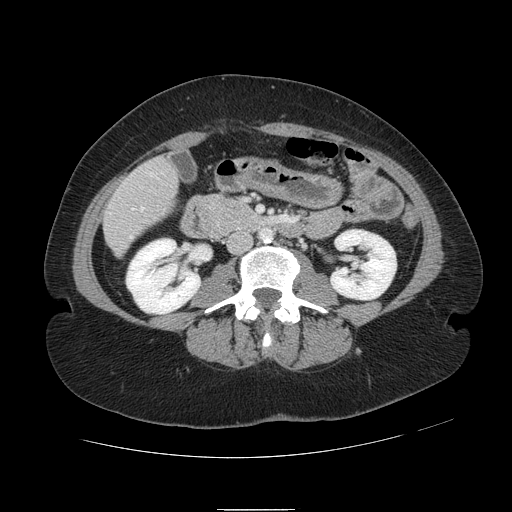
Contrast-enhanced abdominal CT, one axial slice; slice 20 of 121 in the series (ordered by position); 120 kVp; intravenous contrast given; soft-tissue window (W 400 / L 40 HU); 2.5 mm slice thickness; 512 × 512 image matrix, field of view 400 × 400 mm. Female patient, age 52 years. Case-level facts recorded for this patient, not image findings: diagnosis: colorectal cancer liver metastases, imaged before liver resection; multiple liver metastases: yes; largest metastasis: 6.3 cm; disease in both lobes: no.
Structures marked on this image (expert manual segmentation):
- hepatic veins: bounding box [x1, y1, x2, y2] px = [130, 173, 153, 238]
- liver: [105, 161, 176, 253]
- portal vein (with intrahepatic branches): [132, 208, 134, 210]